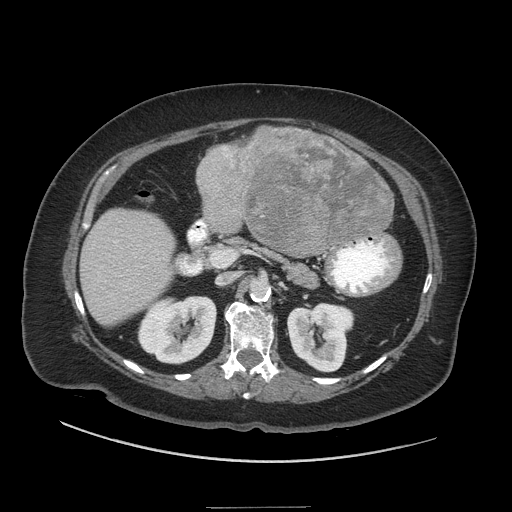
Contrast-enhanced abdominal CT (liver protocol), one axial slice; slice 13 of 81 in the series (ordered by position); reconstruction kernel STANDARD; 140 kVp; soft-tissue window (W 400 / L 40 HU); 512 × 512 image matrix, field of view 440 × 440 mm. Case-level facts recorded for this patient, not image findings: diagnosis: hepatocellular carcinoma (patient treated with transarterial chemoembolisation; whether this scan precedes or follows treatment is not stated here); TNM stage (as recorded): Stage-II; Child-Pugh class: A; tumour differentiation: moderately differentiated; tumour nodularity: multinodular.
Outlined on this slice (semi-automatic segmentation, software-assisted and operator-edited):
- liver parenchyma outside the tumour (the mass and vessels are separate outlines, so this box may not span the whole liver): bounding box <80,128,394,324> (left, top, right, bottom; pixels)
- mass: <195,126,395,255>
- liver vessels: <114,240,160,298>